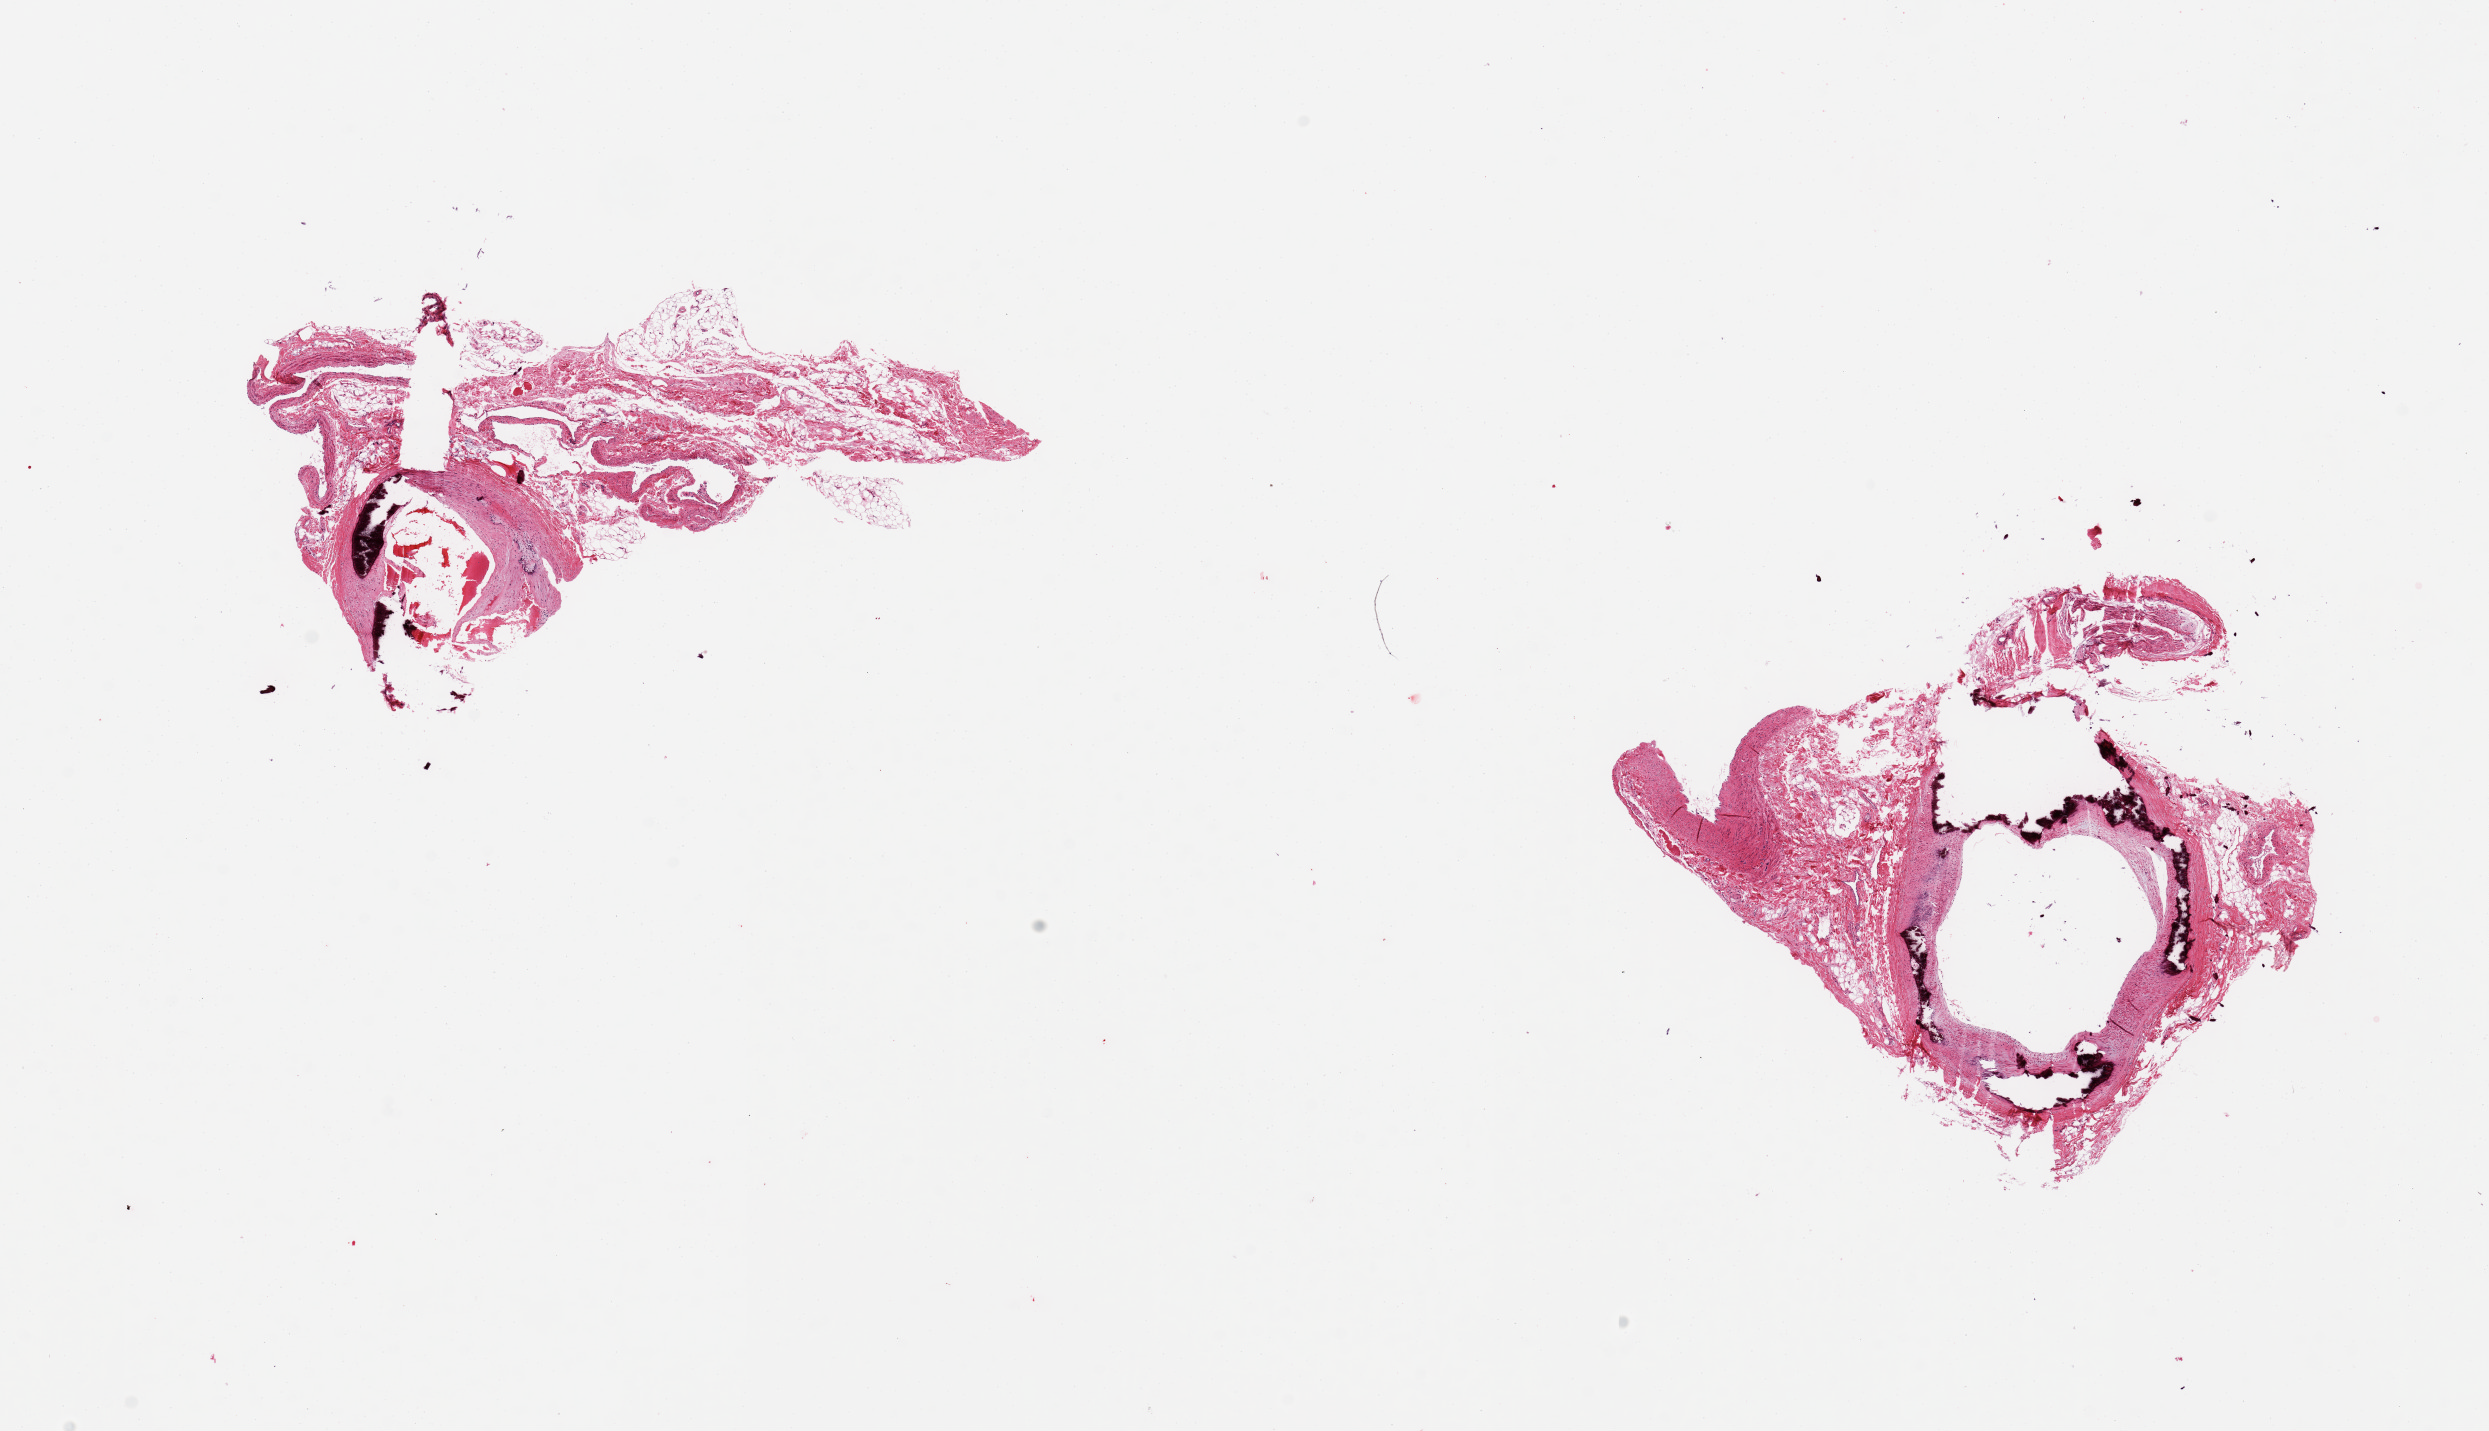
Haematoxylin and eosin whole-slide image, whole scanned area (about 19.7 x 11.3 mm, slide scanned at 20x) shown as a low-resolution overview. PAXgene-fixed paraffin-embedded (PFPE) section. Sampled site (target tissue): tibial artery. Tissue donor sample. Donor: male.
Review note (as recorded): 2 pieces; atherosclerotic plaque and medial calcifications; ~50% attached adventitia and fat.